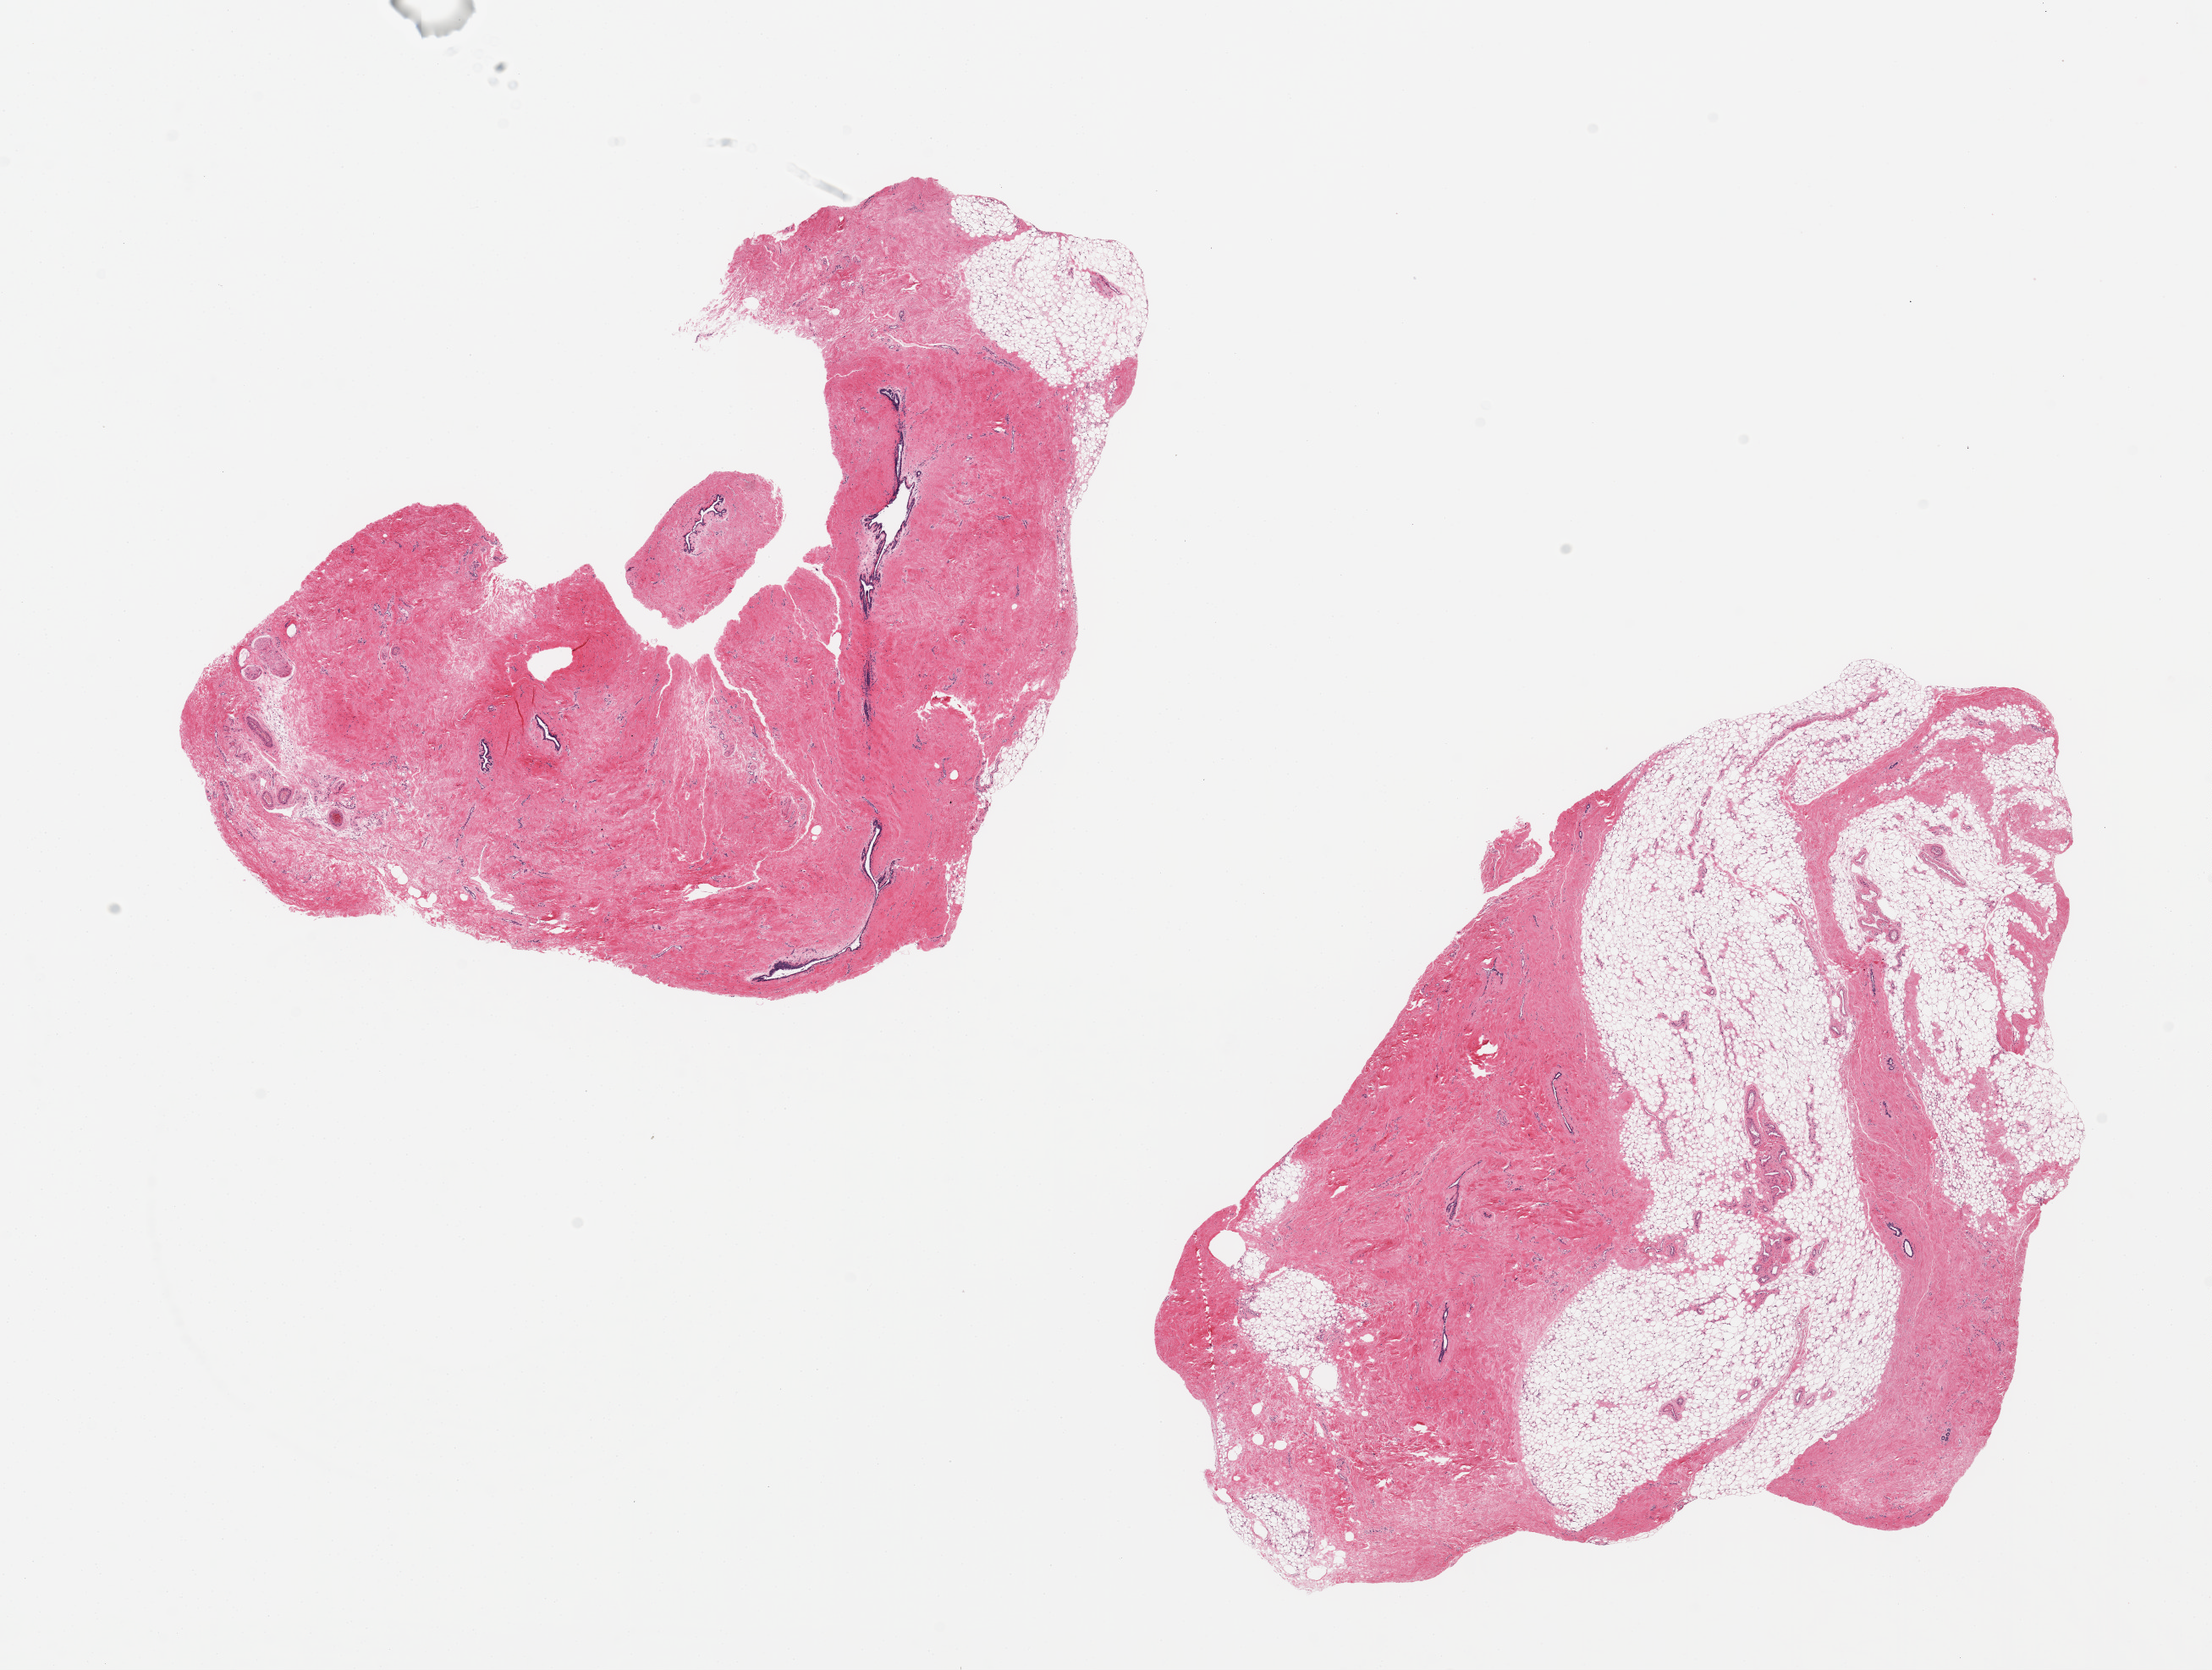
Whole-slide image, haematoxylin and eosin stain — low-resolution overview of the scanned area, about 20.7 x 15.6 mm, PAXgene-fixed, paraffin-embedded tissue, section of breast (target tissue), donor tissue sample. Male donor.
Pathologist's review note for this sample: 2 pieces 10x6.5 & 11x7mm; gynecomastoid hyperplasia.